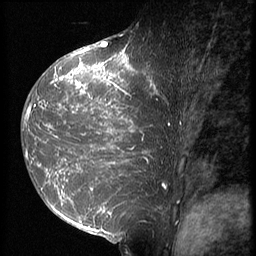
Breast MRI (dynamic contrast-enhanced), one sagittal slice; position 34 of 64 along the scan axis; 3 images stored at this slice position (order not interpretable as contrast timing); 1.5 T; TE 4.2 ms, TR 9 ms; 2.5 mm slice thickness; 256 × 256 image matrix, field of view 180 × 180 mm. Patient: female, 39 years. Case-level facts recorded for this patient, not image findings: setting: breast cancer imaged before/during neoadjuvant chemotherapy; receptor status: HER2-positive.
Annotated regions visible in this slice (semi-automatically segmented with operator editing):
- analysis volume of interest (the breast-tissue region the enhancement analysis was run in; not a lesion): box from (x=23, y=47) to (x=168, y=239) px
- tumour enhancement mask (voxels above the 140 % enhancement threshold inside the analysis volume of interest): (x=24, y=48)–(x=165, y=232)